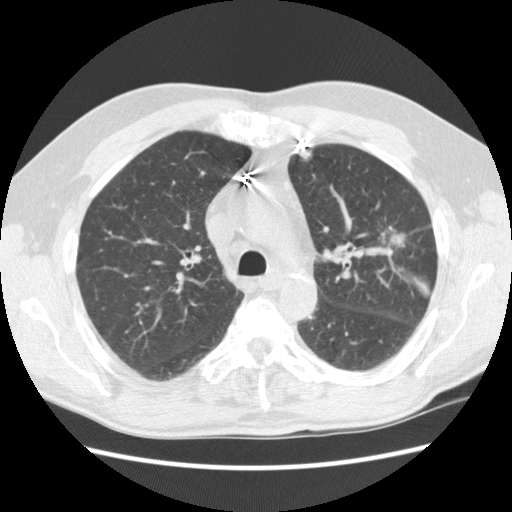
Low-dose screening chest CT, one axial slice; slice 165 of 231 in the series (ordered by position); reconstruction kernel STANDARD; 120 kVp; lung window (W 1500 / L -600 HU); 512 × 512 image matrix, field of view 362 × 362 mm.
Structures marked on this image (manually delineated by an expert):
- lesion 1 (tumor, upper lobe of left lung): bounding box [x1, y1, x2, y2] px = [390, 234, 405, 247]